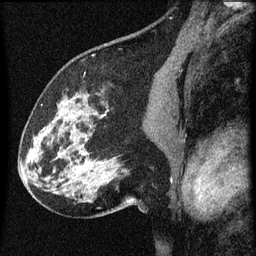
Breast MRI (dynamic contrast-enhanced), one sagittal slice; slice 37 of 60 in the series (ordered by position); dynamic contrast-enhanced series, image 2 of 3 at this slice position (ordered by acquisition); 1.5 T; TE 4.2 ms, TR 8 ms; 2 mm slice thickness; 256 × 256 image matrix. Female patient, age 61 years.
Outlined on this slice (semi-automatic segmentation, software-assisted and operator-edited):
- analysis volume of interest (the breast-tissue region the enhancement analysis was run in; not a lesion): box from (x=27, y=80) to (x=137, y=209) px
- tumour enhancement mask (voxels above the 70 % enhancement threshold inside the analysis volume of interest): (x=32, y=134)–(x=44, y=161)